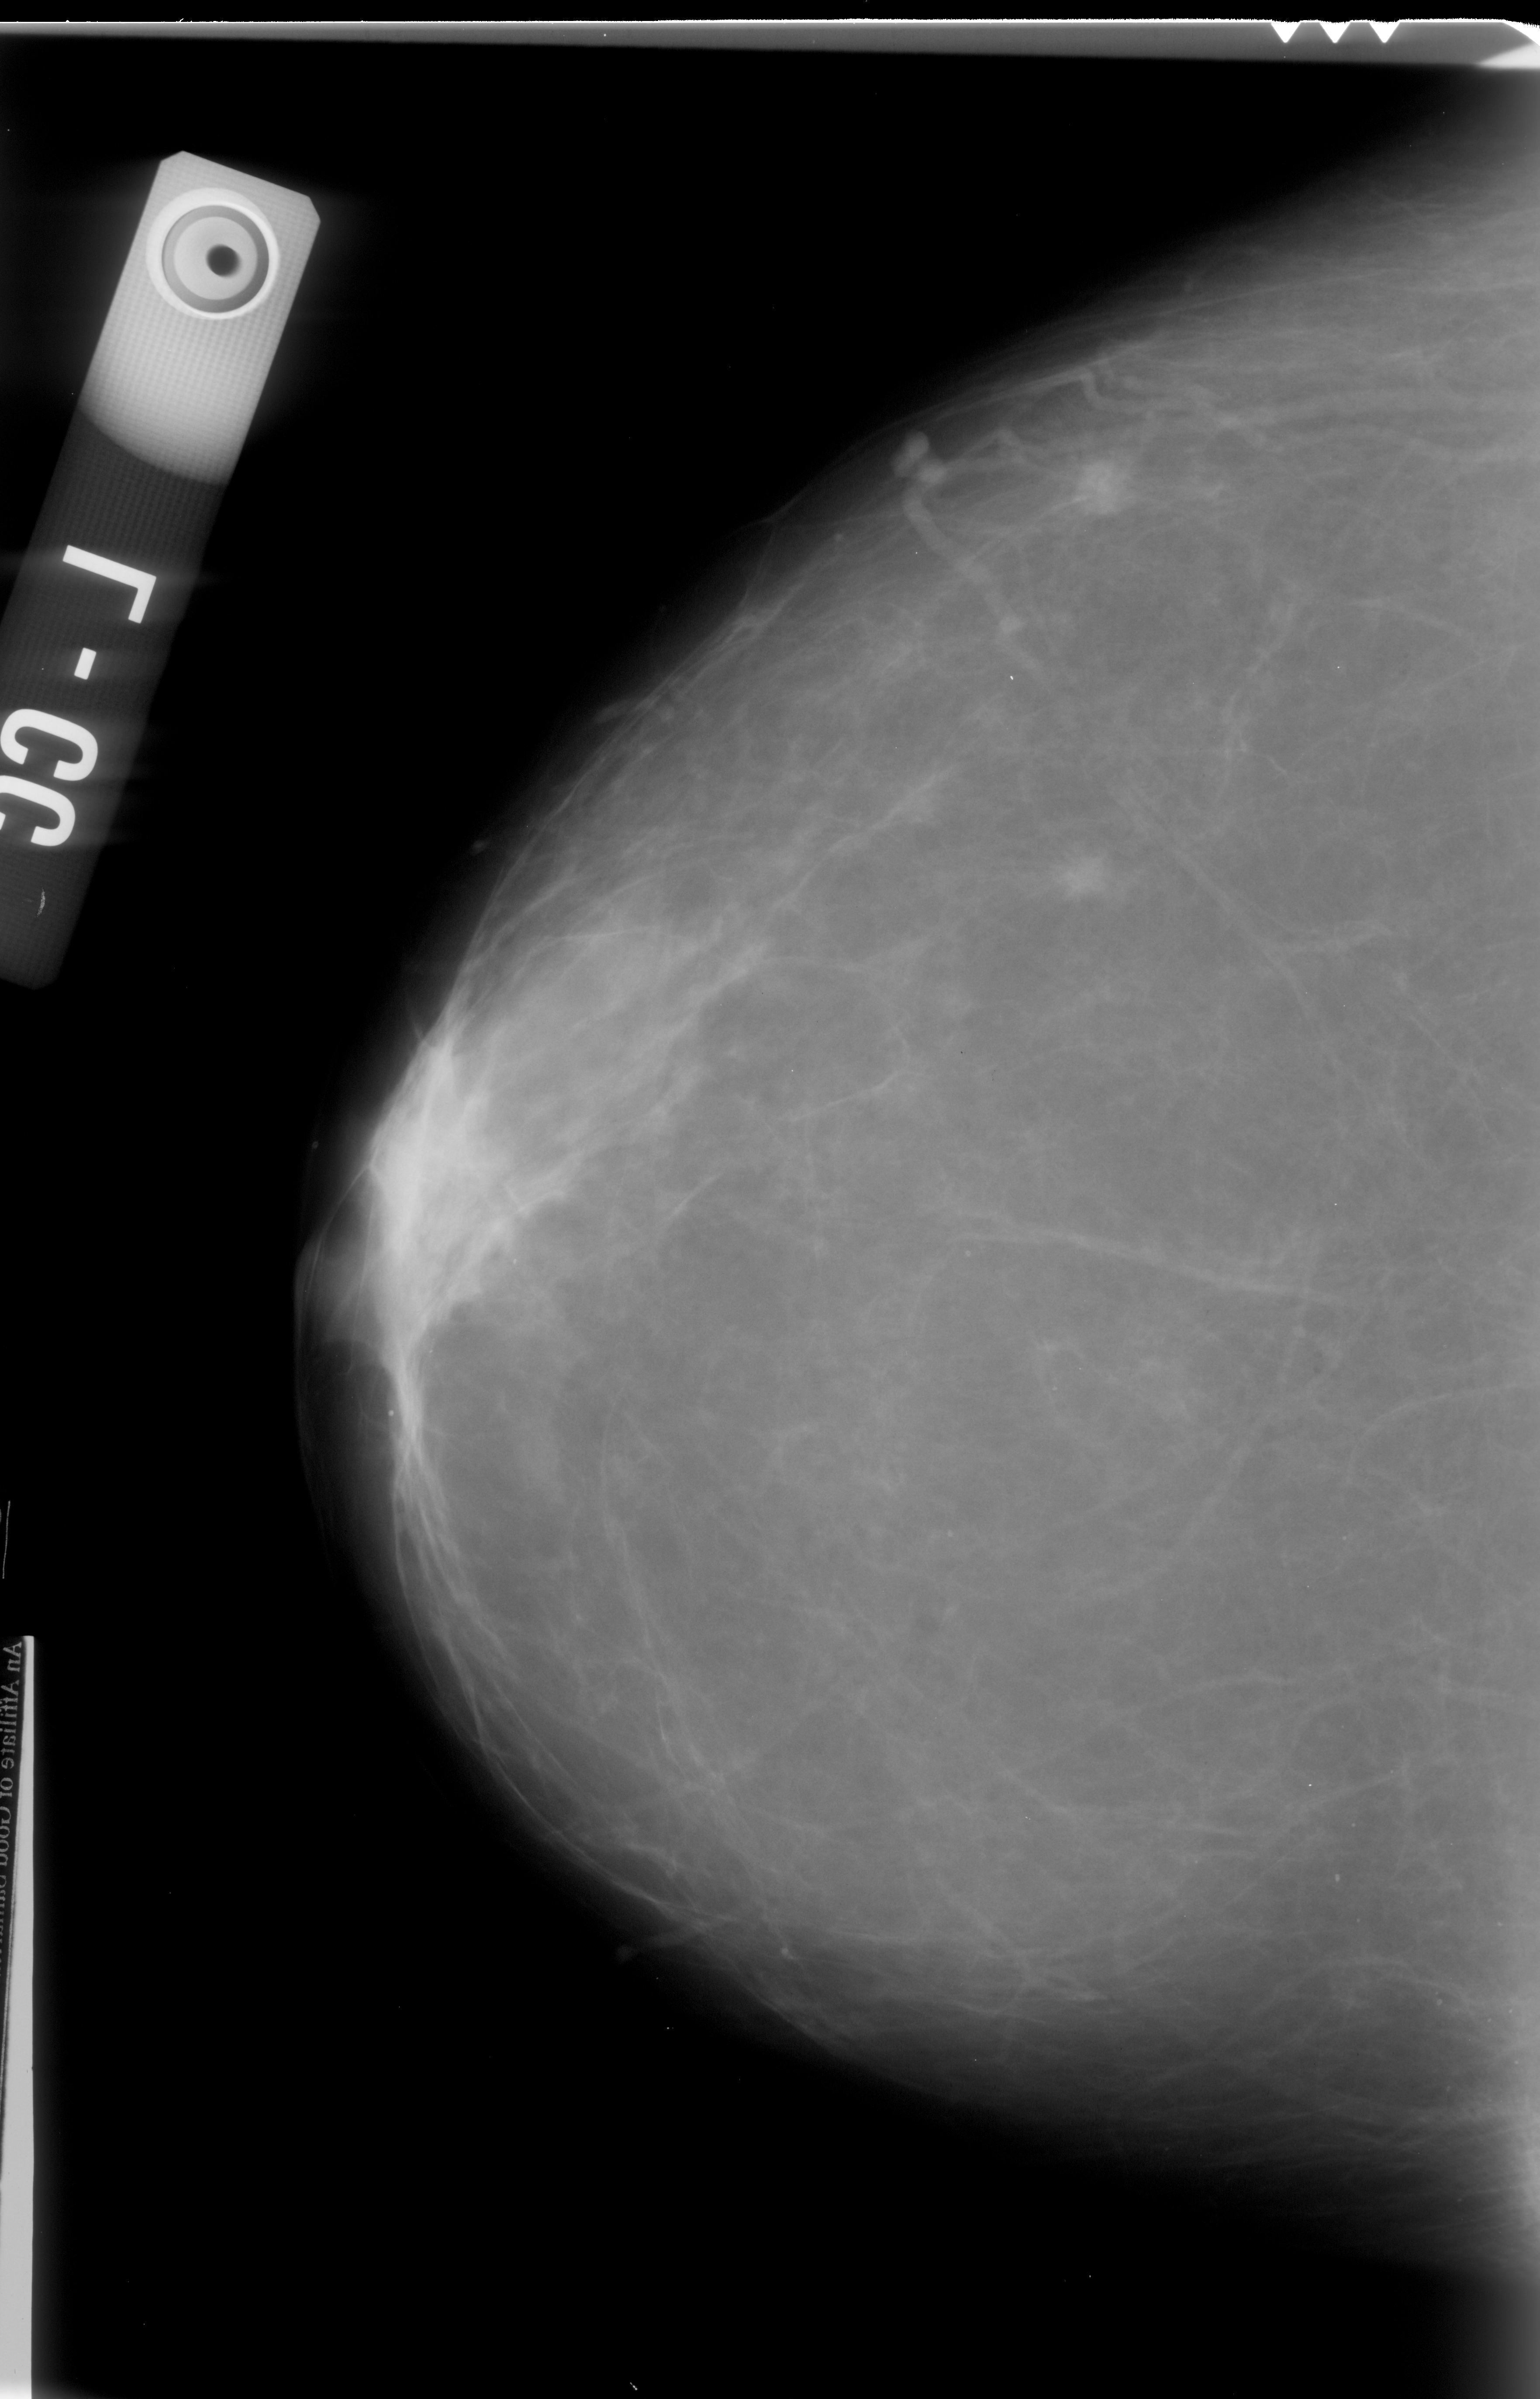
Mammogram (digitized film); left breast; CC view; BI-RADS breast density category 2 (scale 1–4).
Mass, shape irregular, margins spiculated; BI-RADS assessment category 4; pathology (as recorded): malignant.